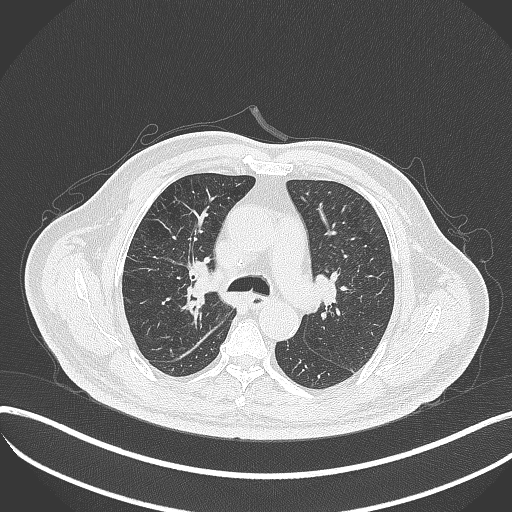
Chest CT, one axial slice. 120 kVp. Lung window (W 1500 / L -600 HU). 1 mm slice thickness. 512 × 512 image matrix. Patient: male, 72 years. Case-level facts recorded for this patient, not image findings: clinical TNM (as recorded): T1c N0 M0; histopathological grade: G2.
Outlined on this slice (rectangle marked by the reading radiologist):
- lung tumour (recorded histology: squamous cell carcinoma): bounding box (x1, y1, x2, y2) in pixels: (185, 257, 212, 304)